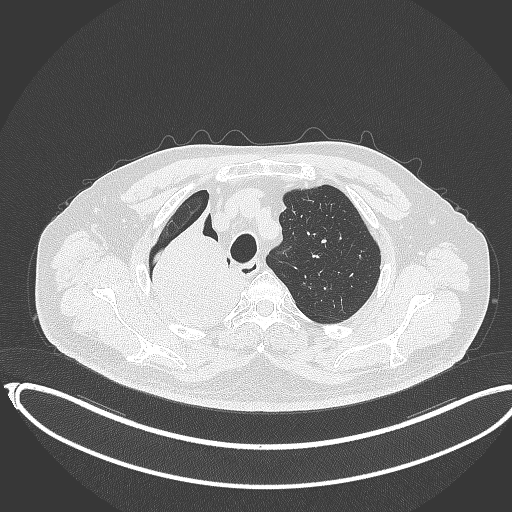
Chest CT, one axial slice. Slice 298 of 403 in the series (ordered by position). Lung window (W 1500 / L -600 HU). 512 × 512 image matrix, field of view 436 × 436 mm. Male patient, age 68 years. From the clinical record (not read from this slice): clinical TNM (as recorded): T2a N0 M0.
Structures marked on this image (bounding box drawn by a radiologist):
- lung tumour (recorded histology: adenocarcinoma): box from (x=134, y=201) to (x=245, y=334) px